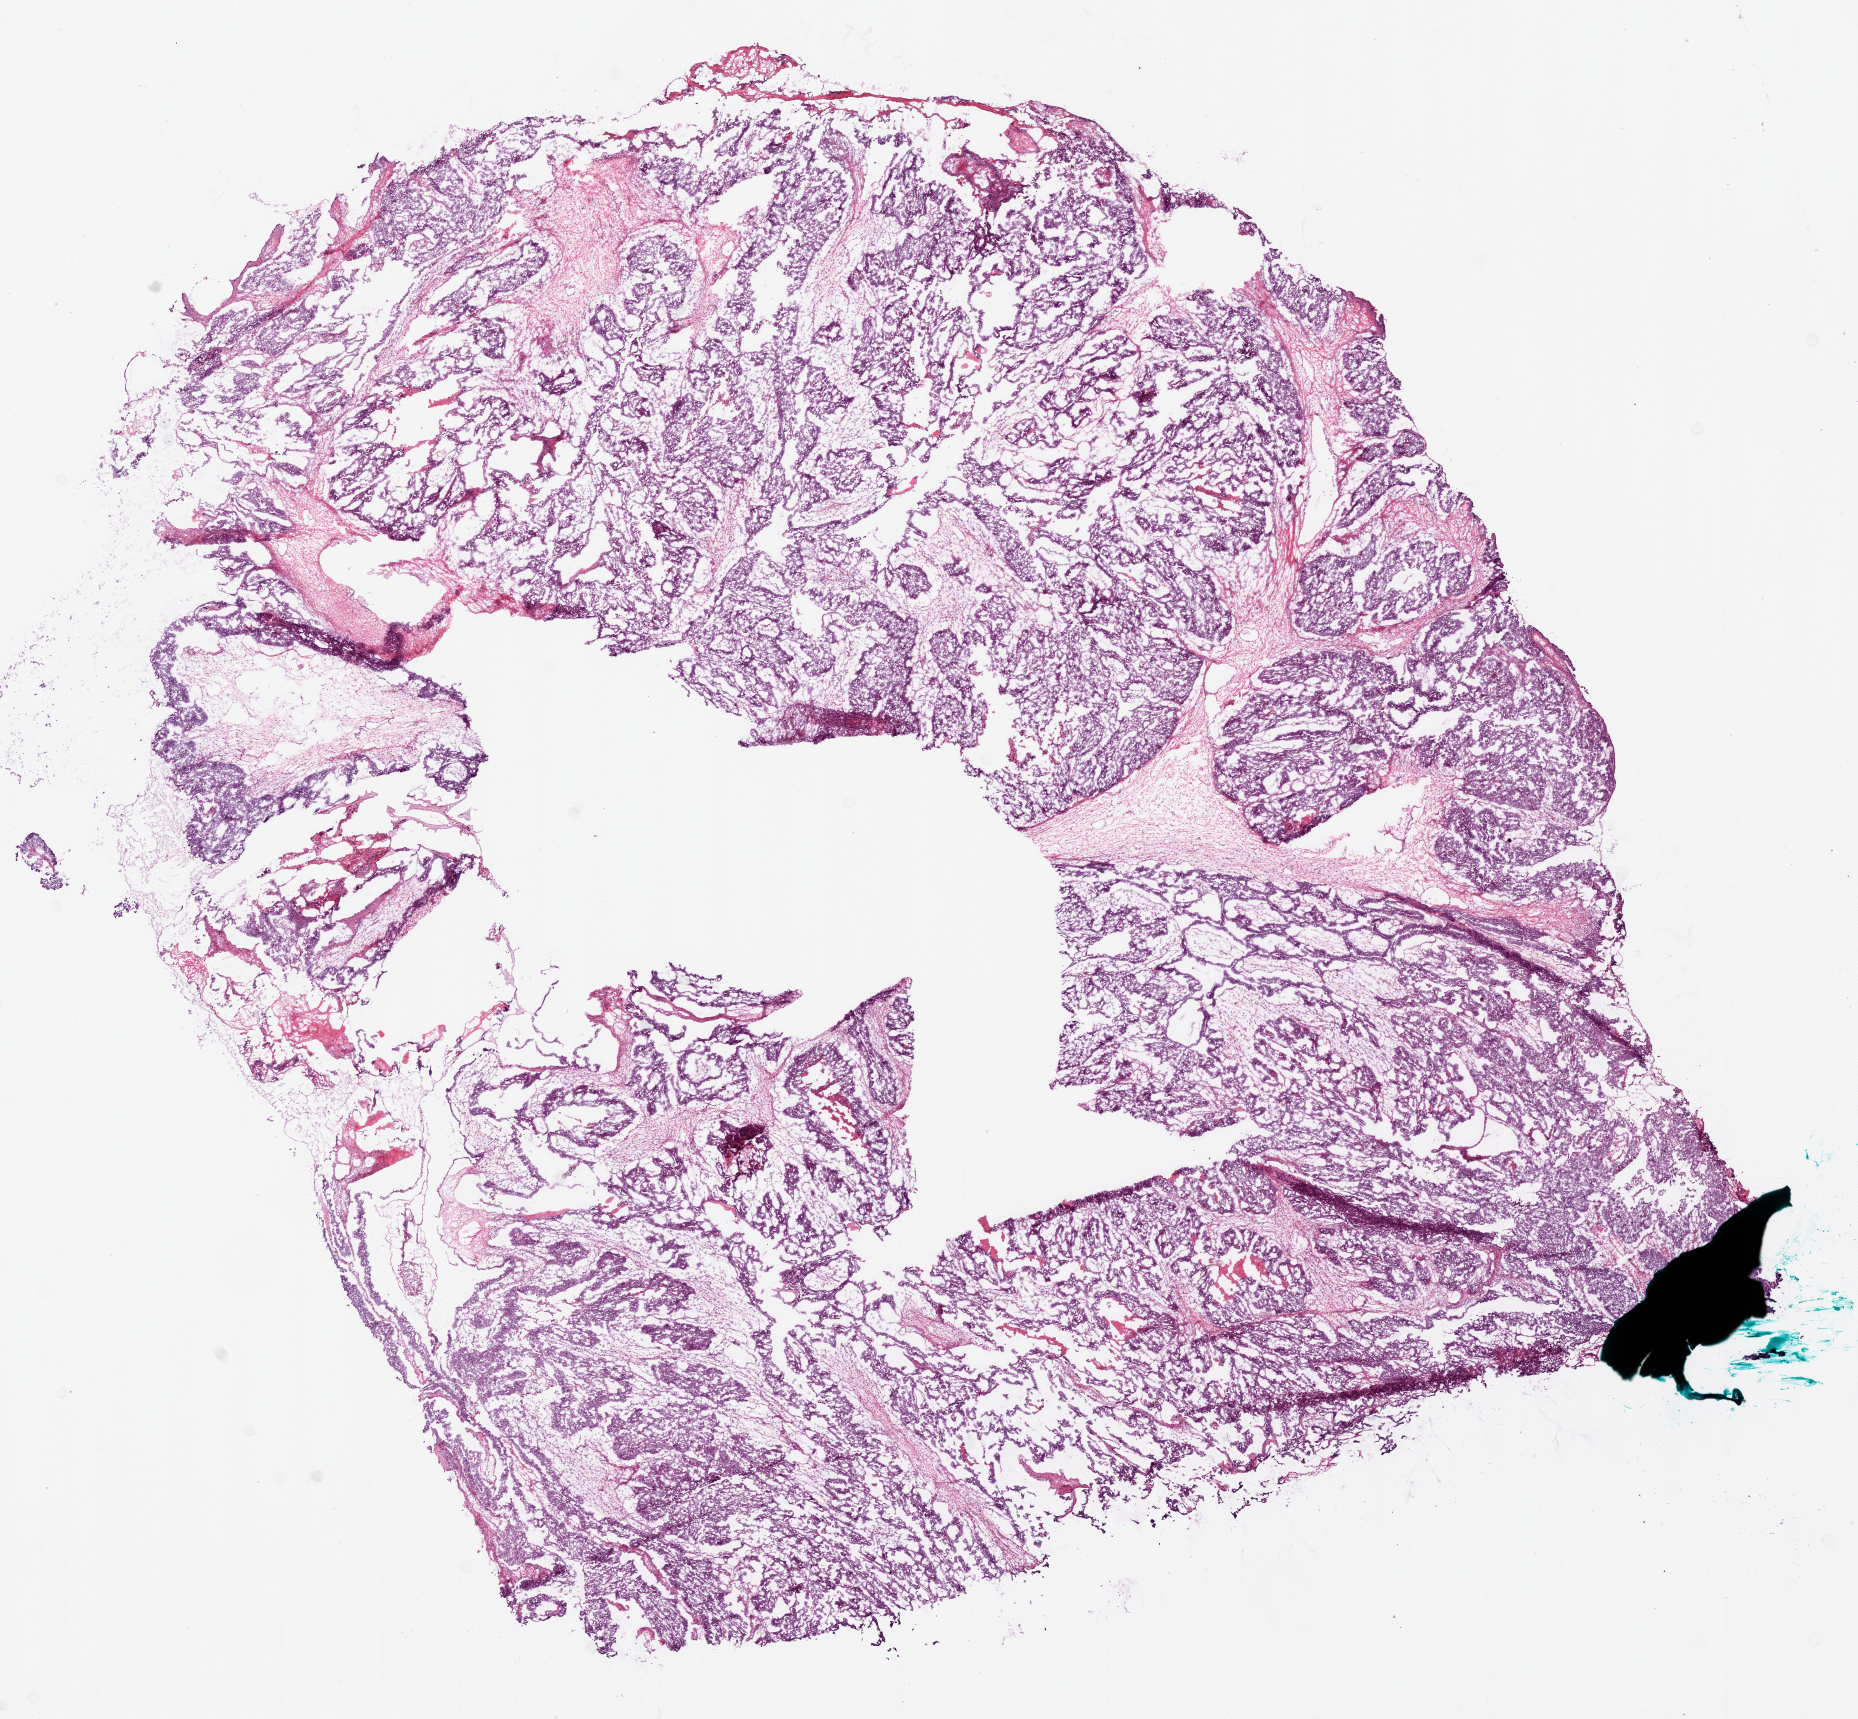
Digitized Hematoxylin and eosin (H&E) stained tissue section (whole slide), whole scanned area (about 14.9 x 13.8 mm, acquisition: 20x scan) shown as a low-resolution overview, frozen section from the bottom of the tissue portion, sample: primary tumour, ovary. Patient: female, age at initial diagnosis 52 years. Histologic grade: G3 (poorly differentiated). Slide review estimates, as recorded: tumour cells 60%, tumour nuclei 80%, normal cells 0%, stromal cells 35%, necrosis 5%.
Laterality: bilateral. Histologic diagnosis: Serous cystadenocarcinoma, NOS. FIGO stage: IIIC.